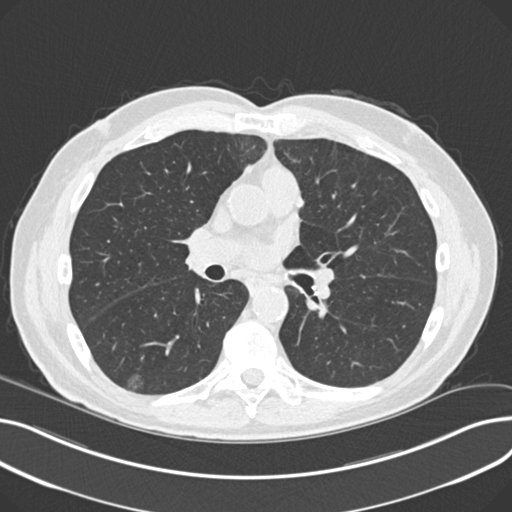
Low-dose screening chest CT, one axial slice; slice 119 of 230 in the series (ordered by position); 120 kVp; lung window (W 1500 / L -600 HU); 2 mm slice thickness; 512 × 512 image matrix.
Structures marked on this image (outlined manually by an expert reader):
- lesion 1 (nodule, lower lobe of right lung): bounding box <127,376,144,394> (left, top, right, bottom; pixels)